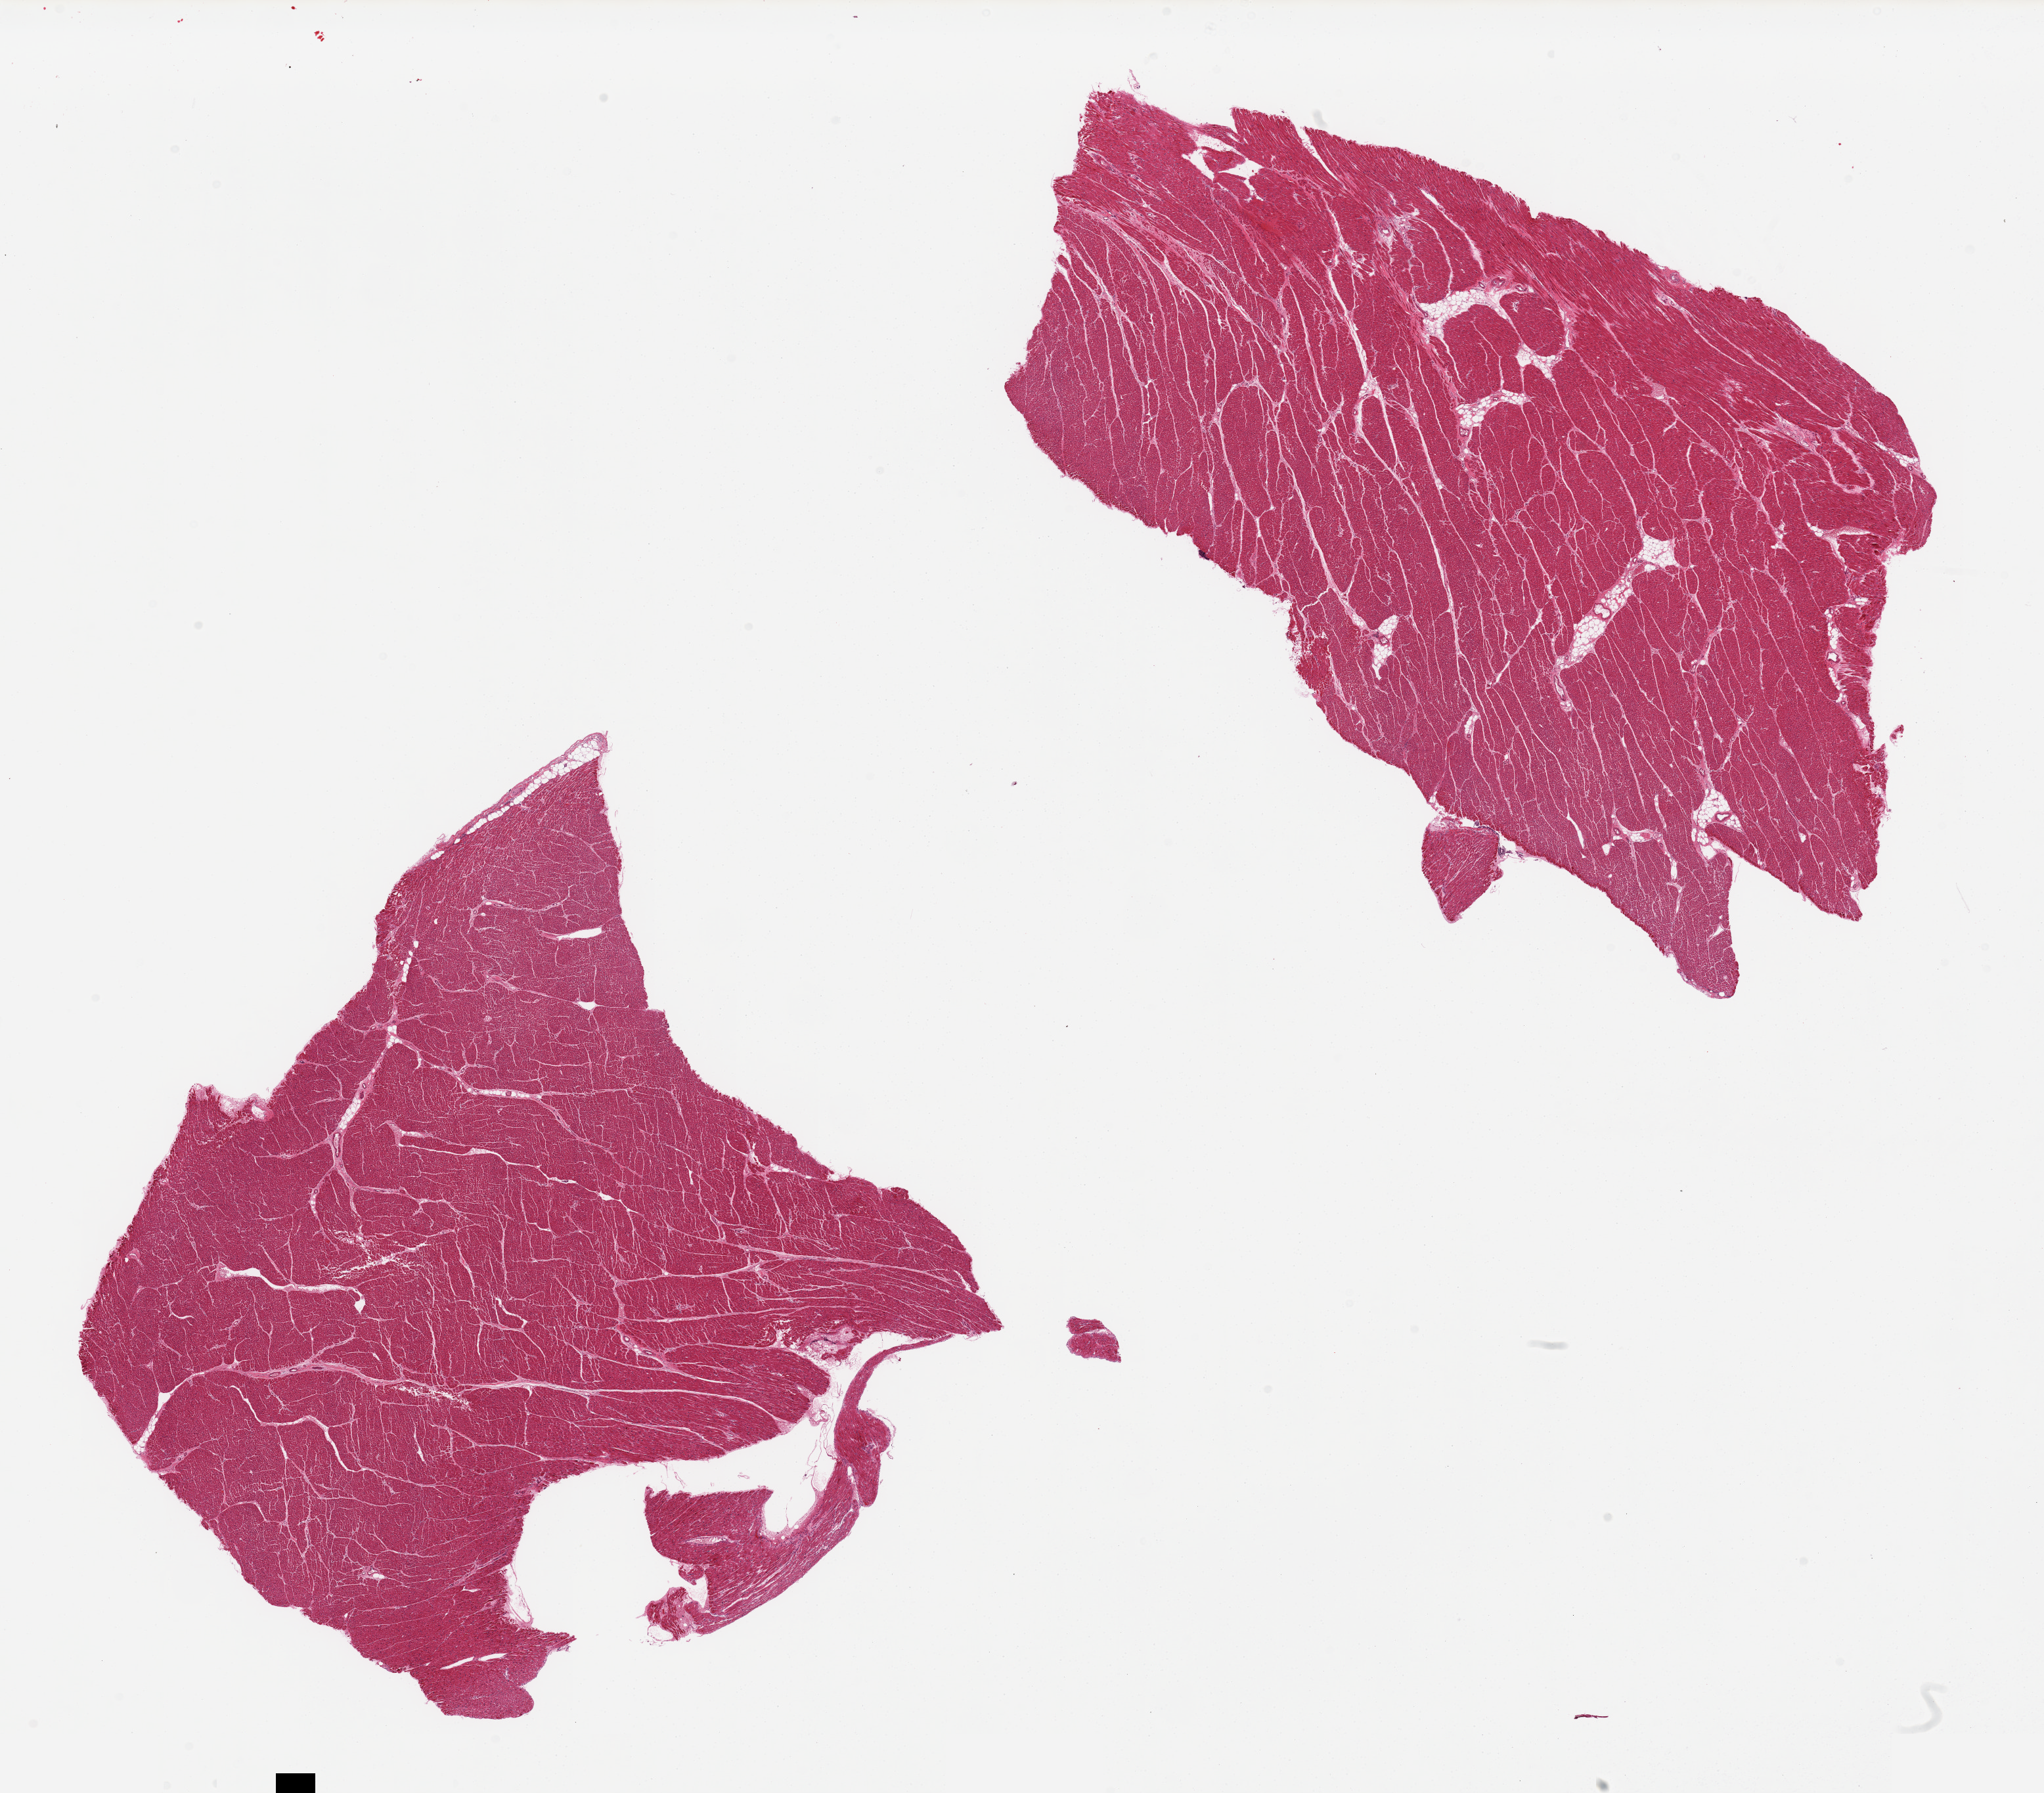
H&E whole-slide image — shown as a low-resolution overview of the whole scanned area (about 24.6 x 21.6 mm, from a 20x scan), PAXgene-fixed paraffin-embedded (PFPE) section, target tissue: heart, donor tissue sample. Donor sex: female.
Review note (as recorded): 2 pieces, minimal ischemic changes.